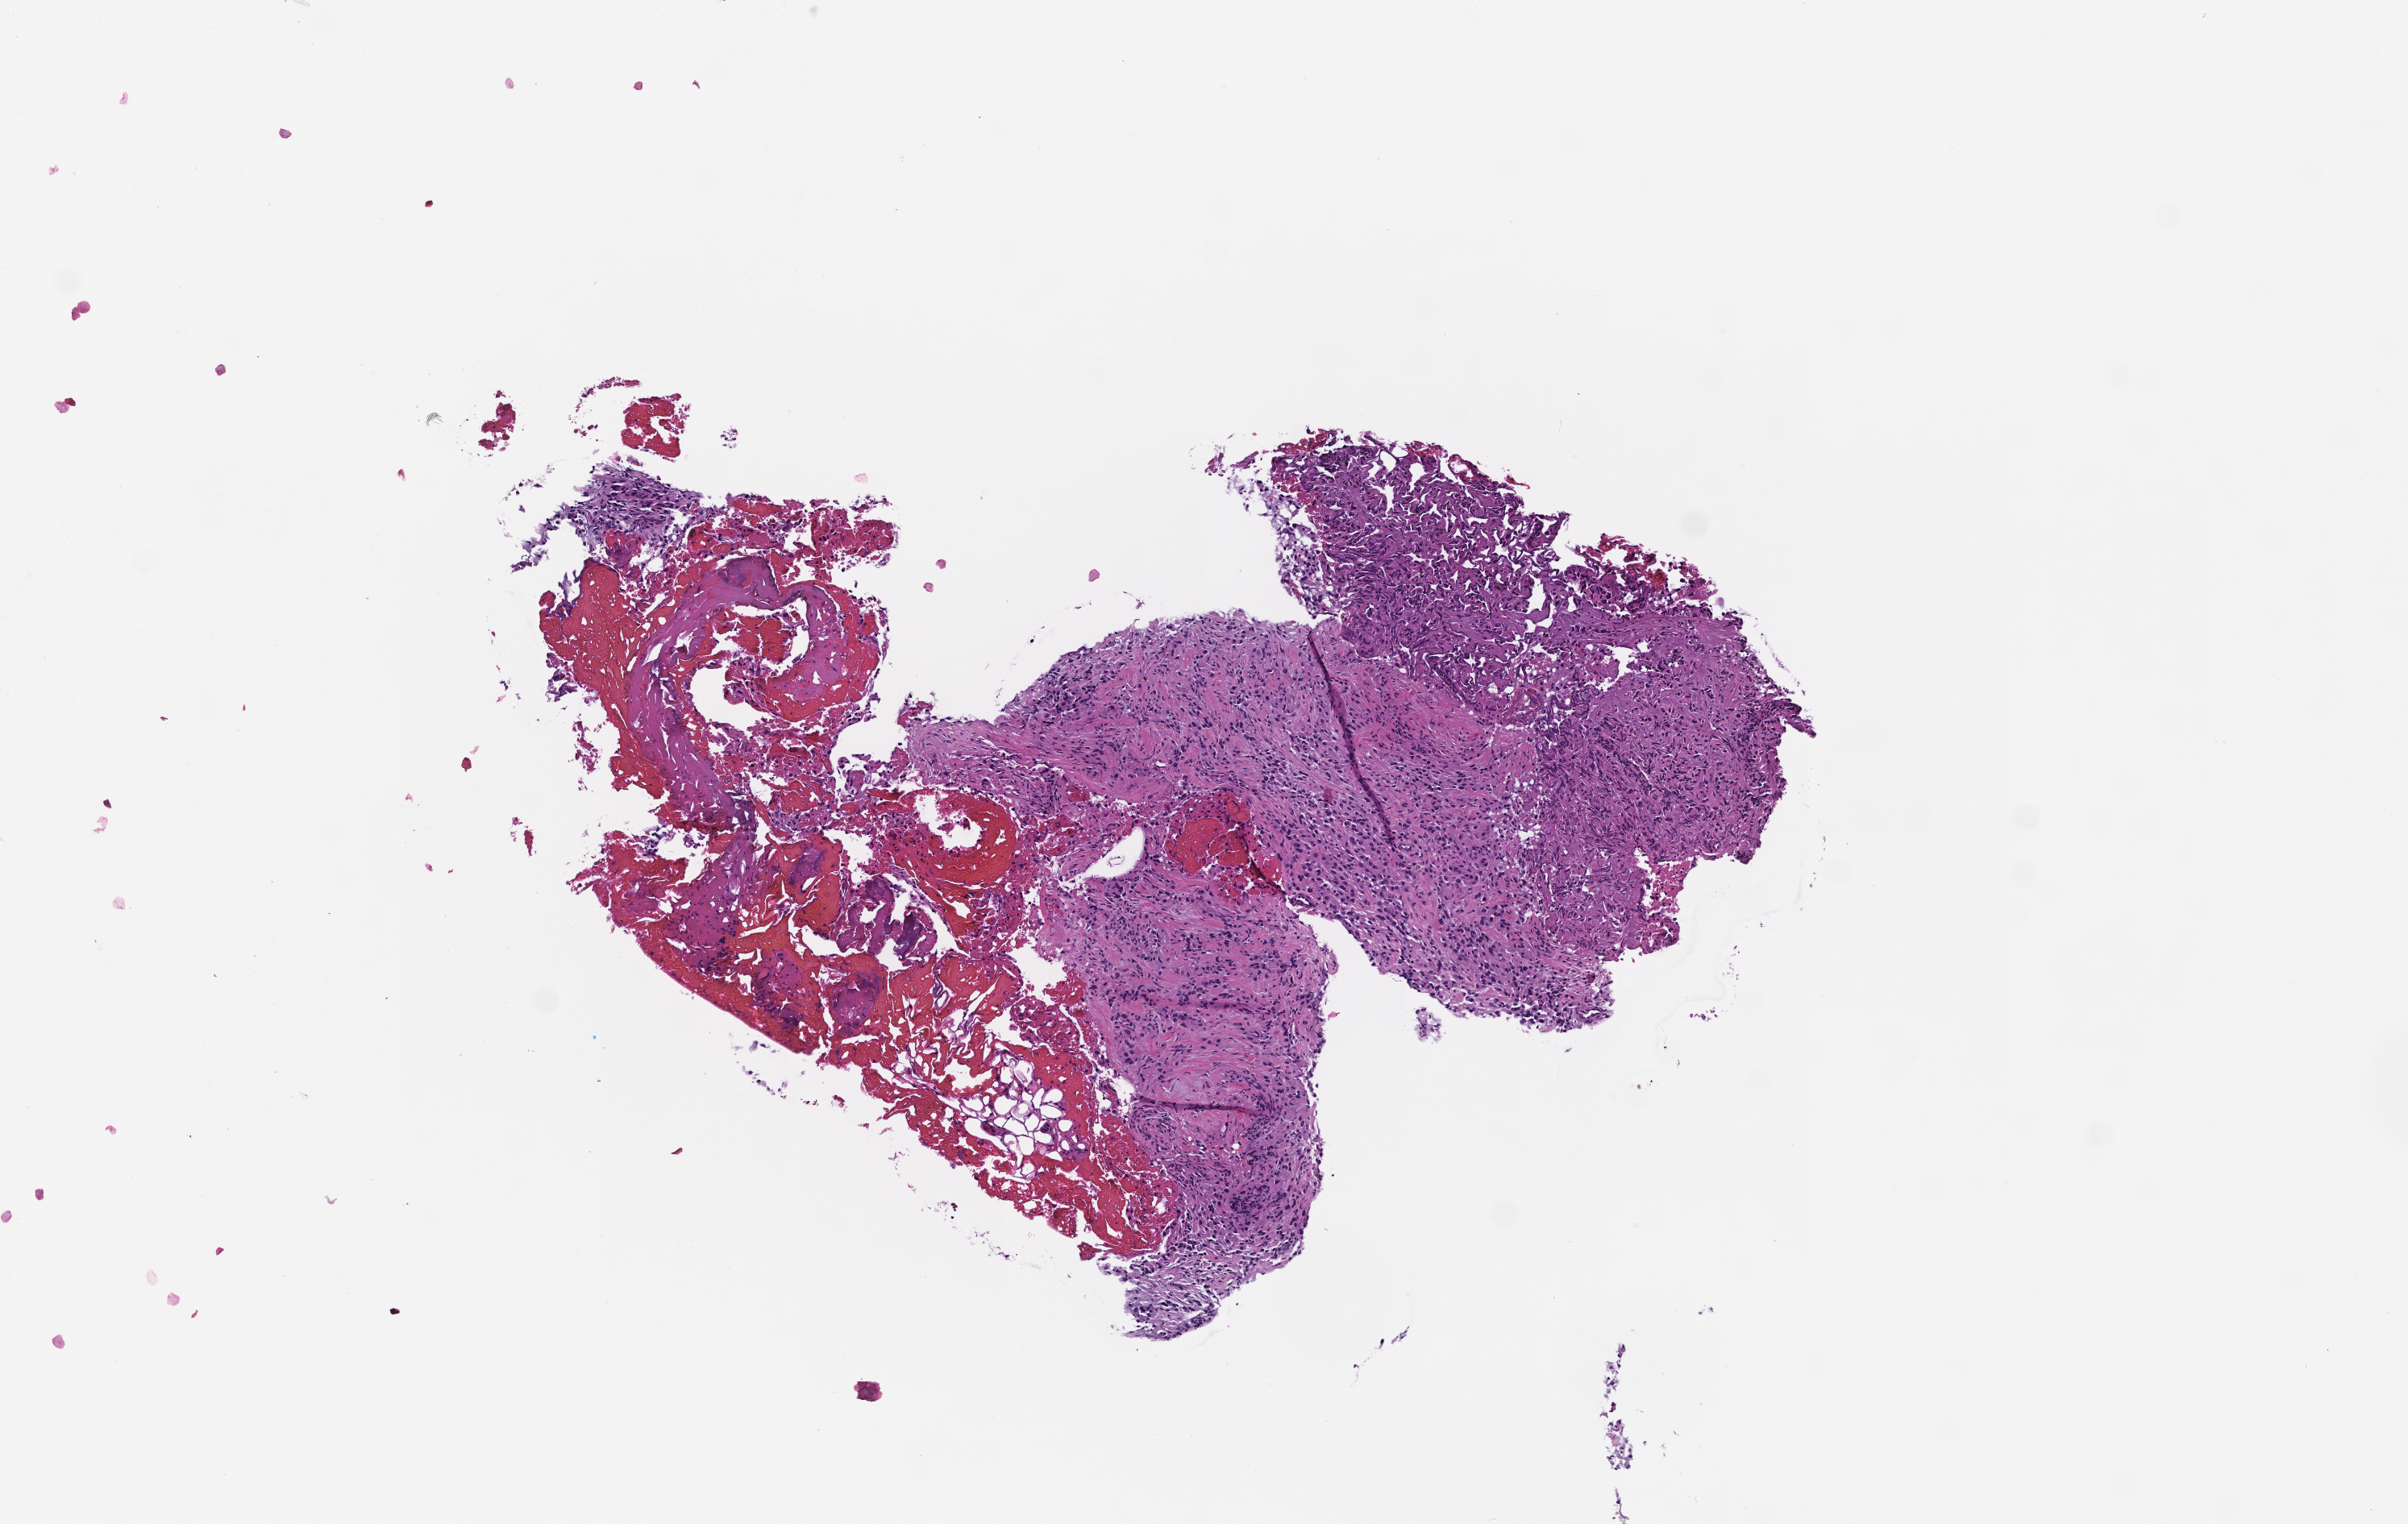
Whole-slide image, hematoxylin and eosin (H&E) stain — low-resolution overview of the scanned area, about 6.0 x 3.8 mm, FFPE section, specimen time point: collected at disease progression. Patient sex: female.
This section: metastatic tumor tissue. Primary diagnosis of the patient: Non-Small Cell Lung Carcinoma.